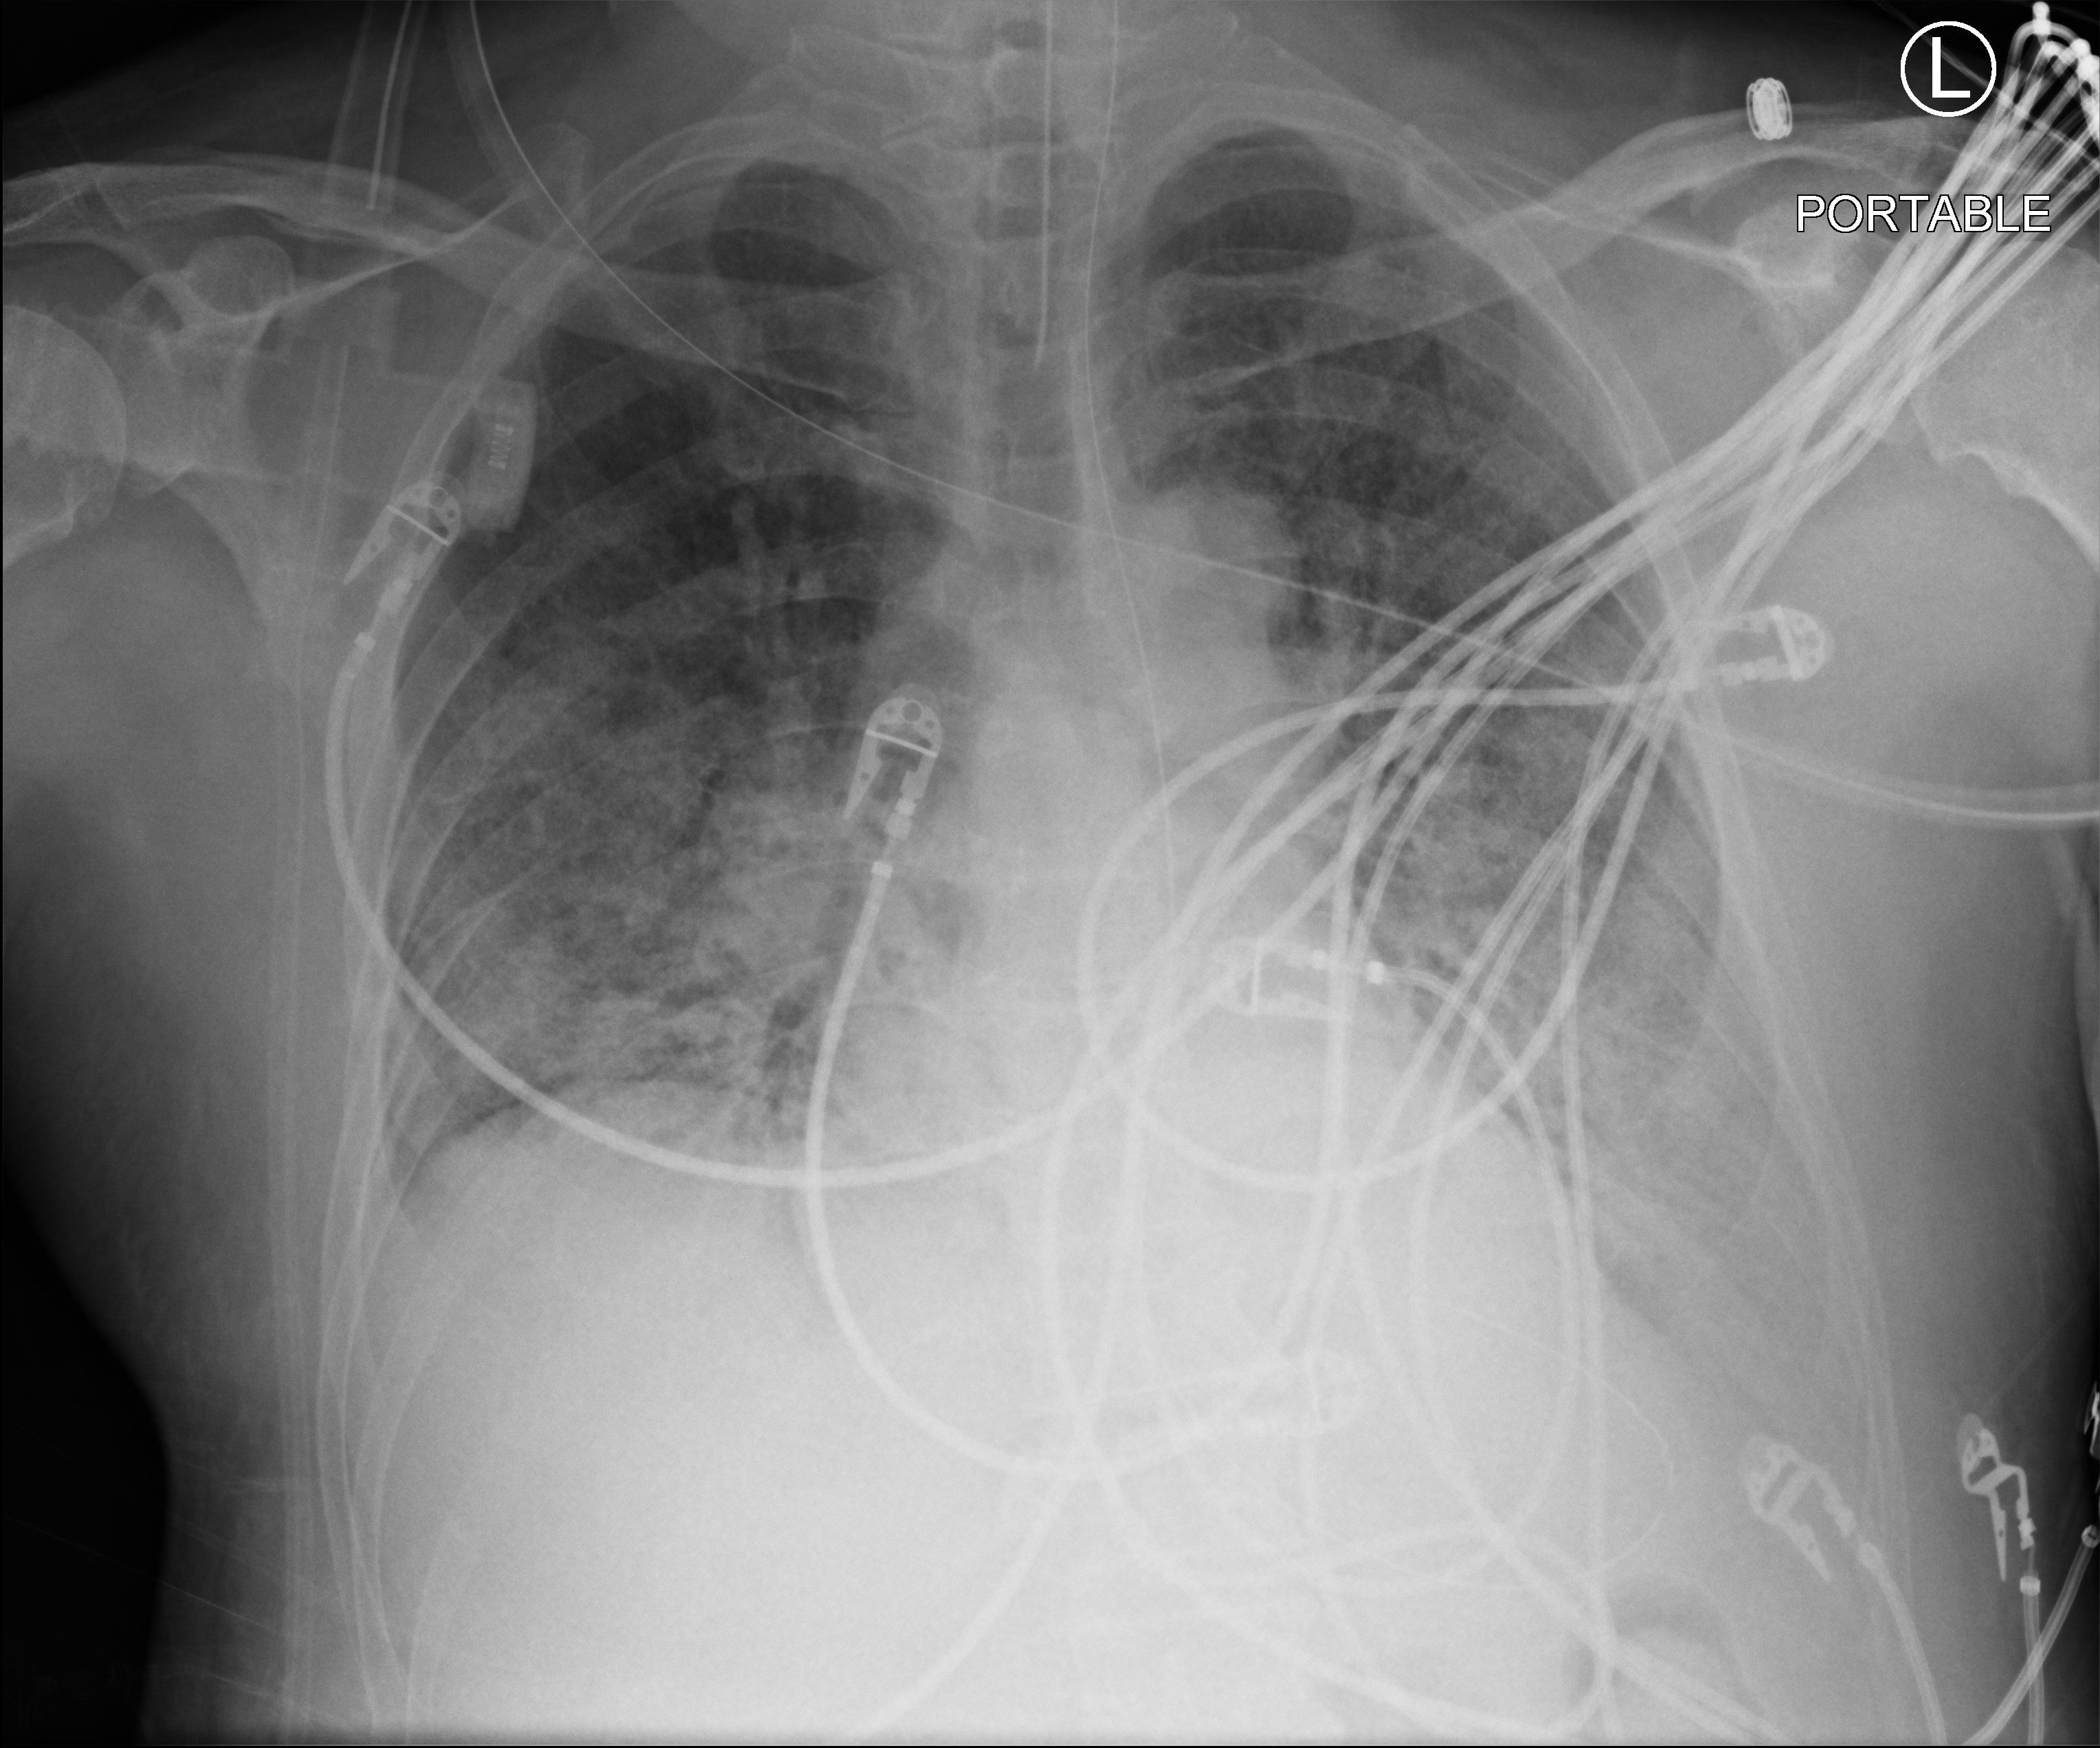
Bedside chest radiograph (computed radiography). Patient hospitalised with COVID-19; male, aged 60–74 years.
Hospital-stay facts (about this admission, not read from this image; timing relative to this image not recorded):
- admitted to intensive care during this hospital stay: yes